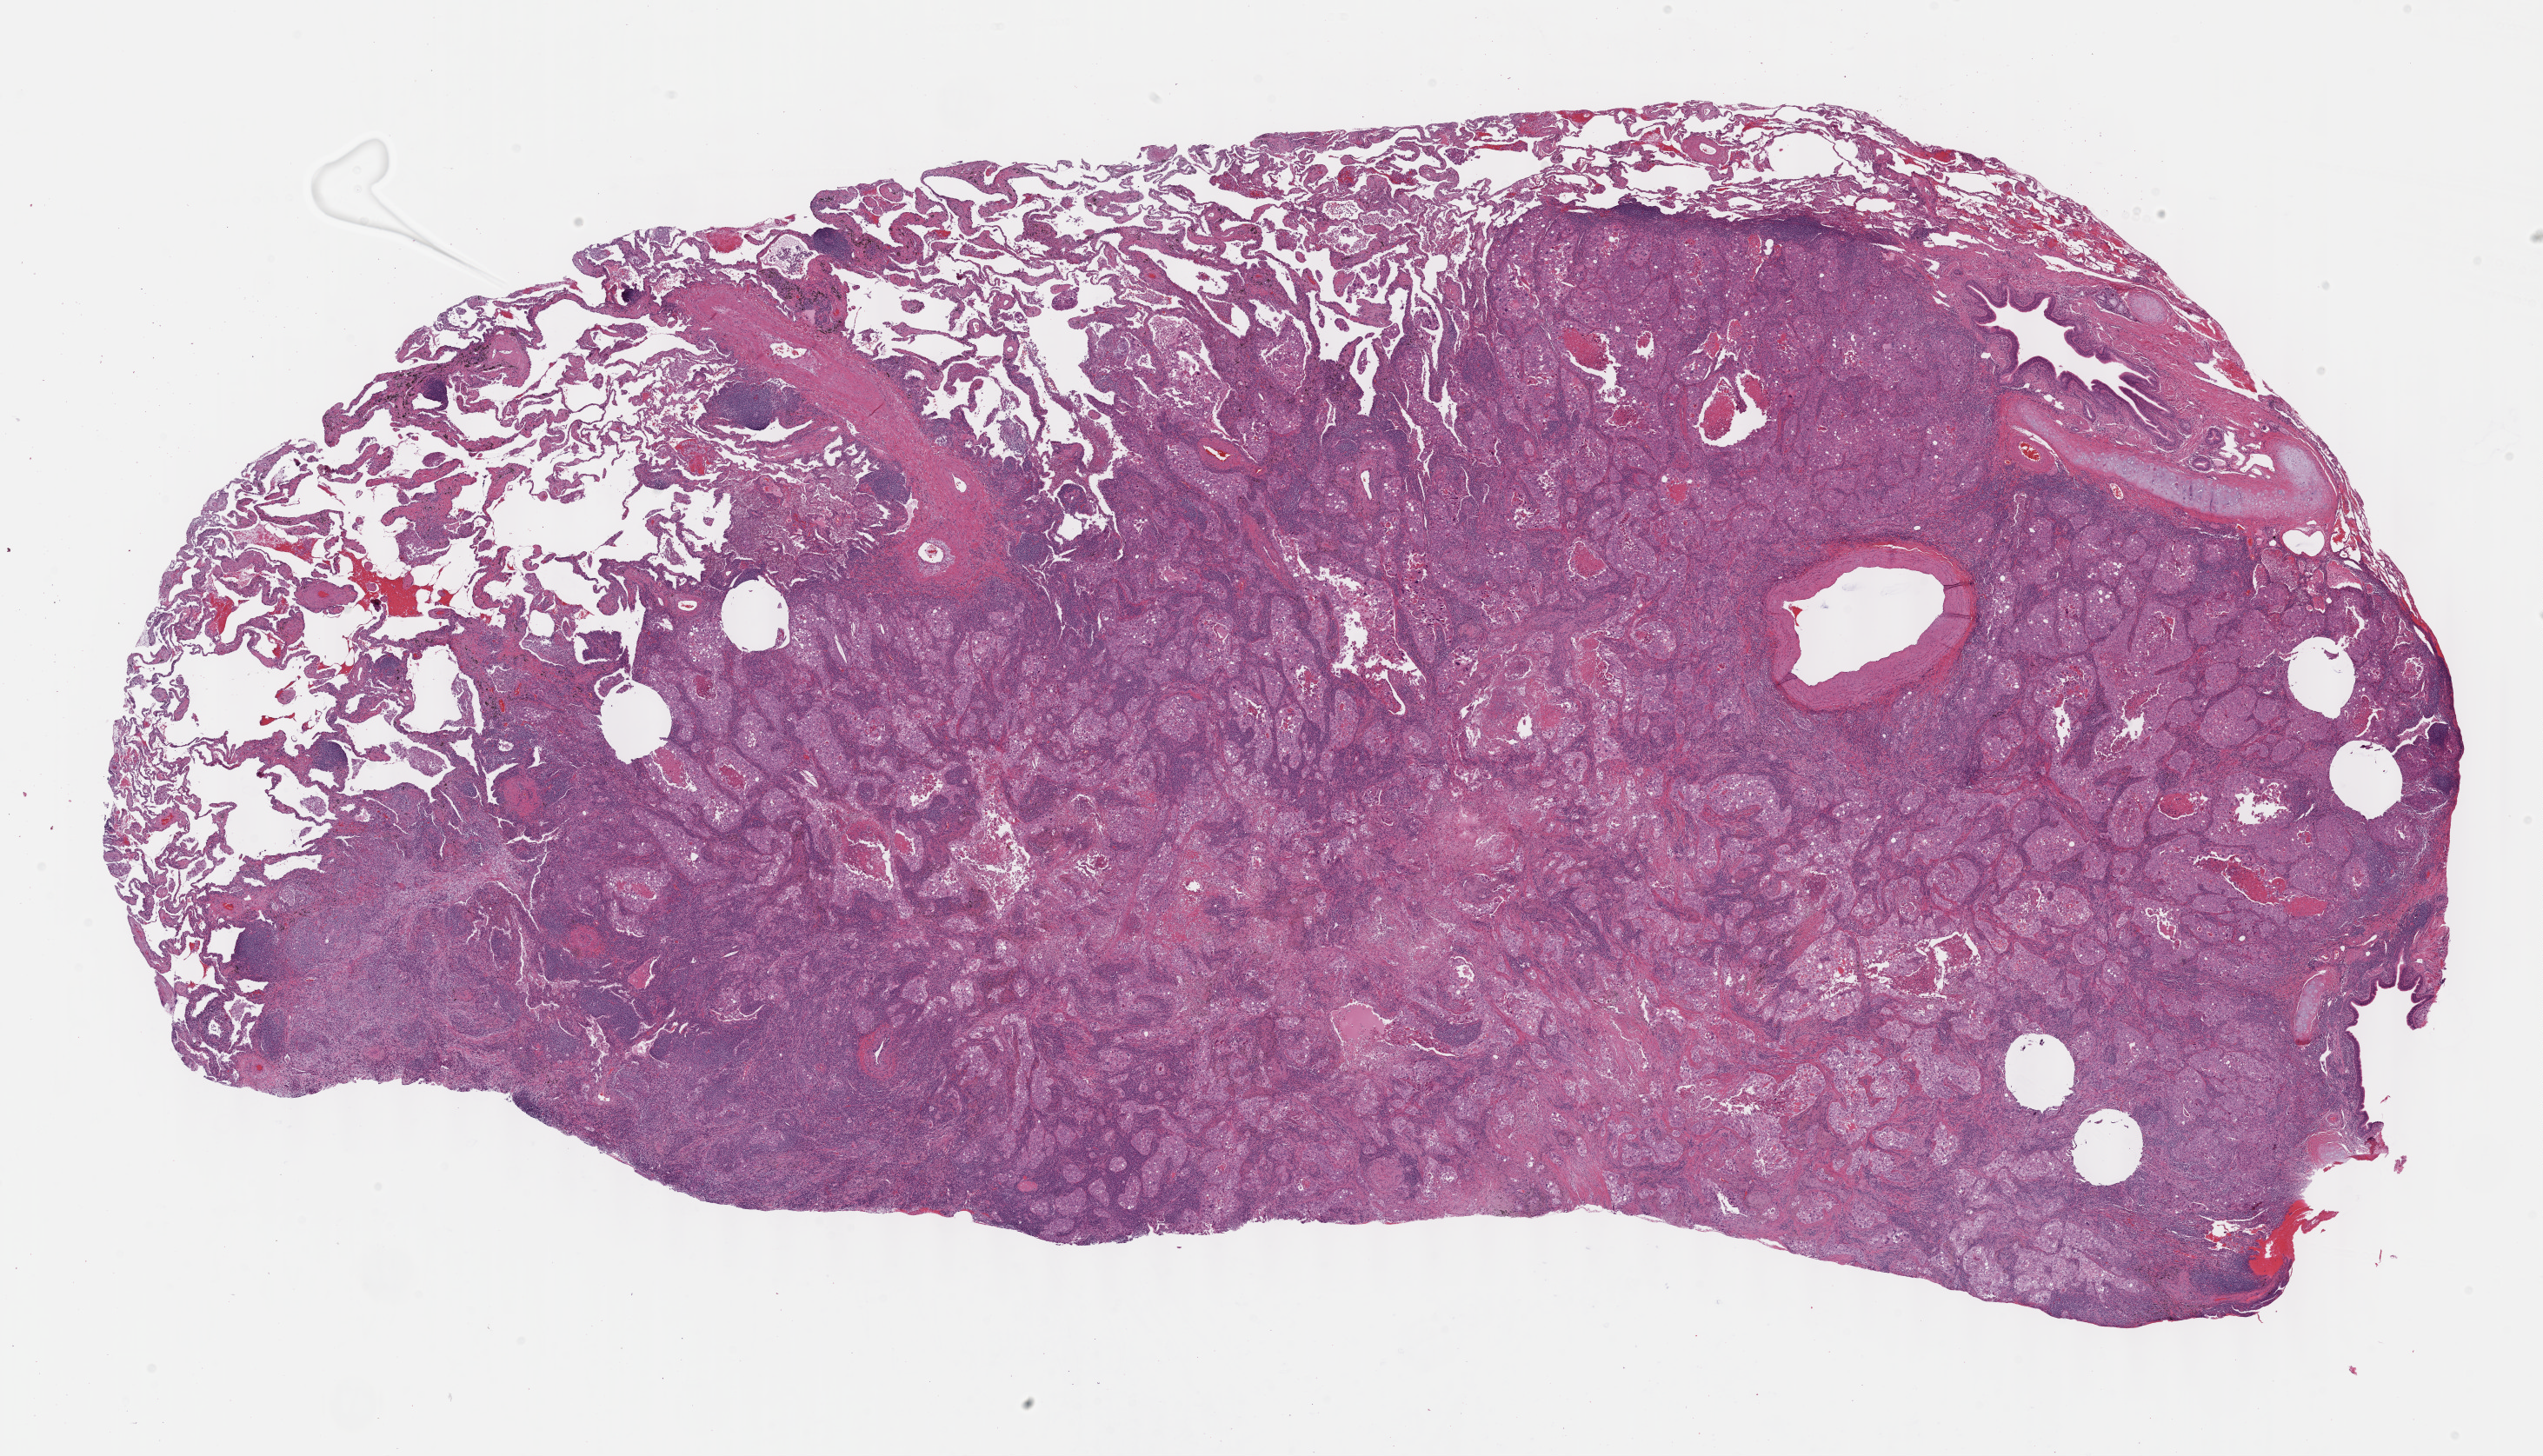
Digitized H&E-stained tissue section (whole slide), low-resolution overview of the scanned area, about 23.6 x 13.5 mm. FFPE section. Primary tumour sample from the lung. Male patient; age at initial diagnosis 63 years.
AJCC pathologic stage: IA. Diagnosis: Squamous cell carcinoma, NOS.